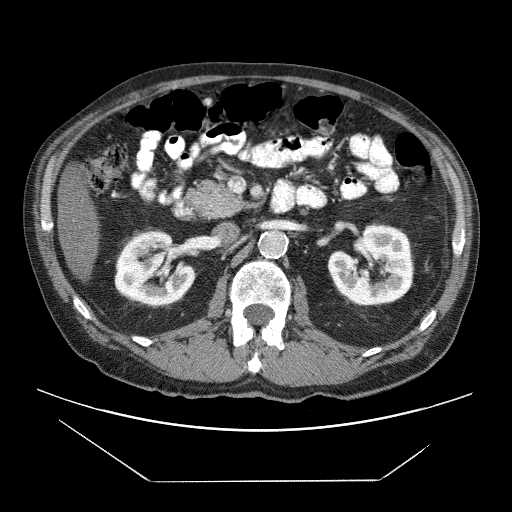
Contrast-enhanced abdominal CT (liver protocol), one axial slice. Position 14 of 83 along the scan axis. Reconstruction kernel STANDARD. Soft-tissue window (W 400 / L 40 HU). 512 × 512 image matrix, field of view 420 × 420 mm. Case-level facts recorded for this patient, not image findings: diagnosis: hepatocellular carcinoma (patient treated with transarterial chemoembolisation; whether this scan precedes or follows treatment is not stated here); TNM stage (as recorded): Stage-IVB; Child-Pugh class: B; tumour nodularity: uninodular.
Annotated regions visible in this slice (semi-automatically segmented with operator editing):
- liver parenchyma outside the tumour (the mass and vessels are separate outlines, so this box may not span the whole liver): box from (x=58, y=184) to (x=100, y=280) px